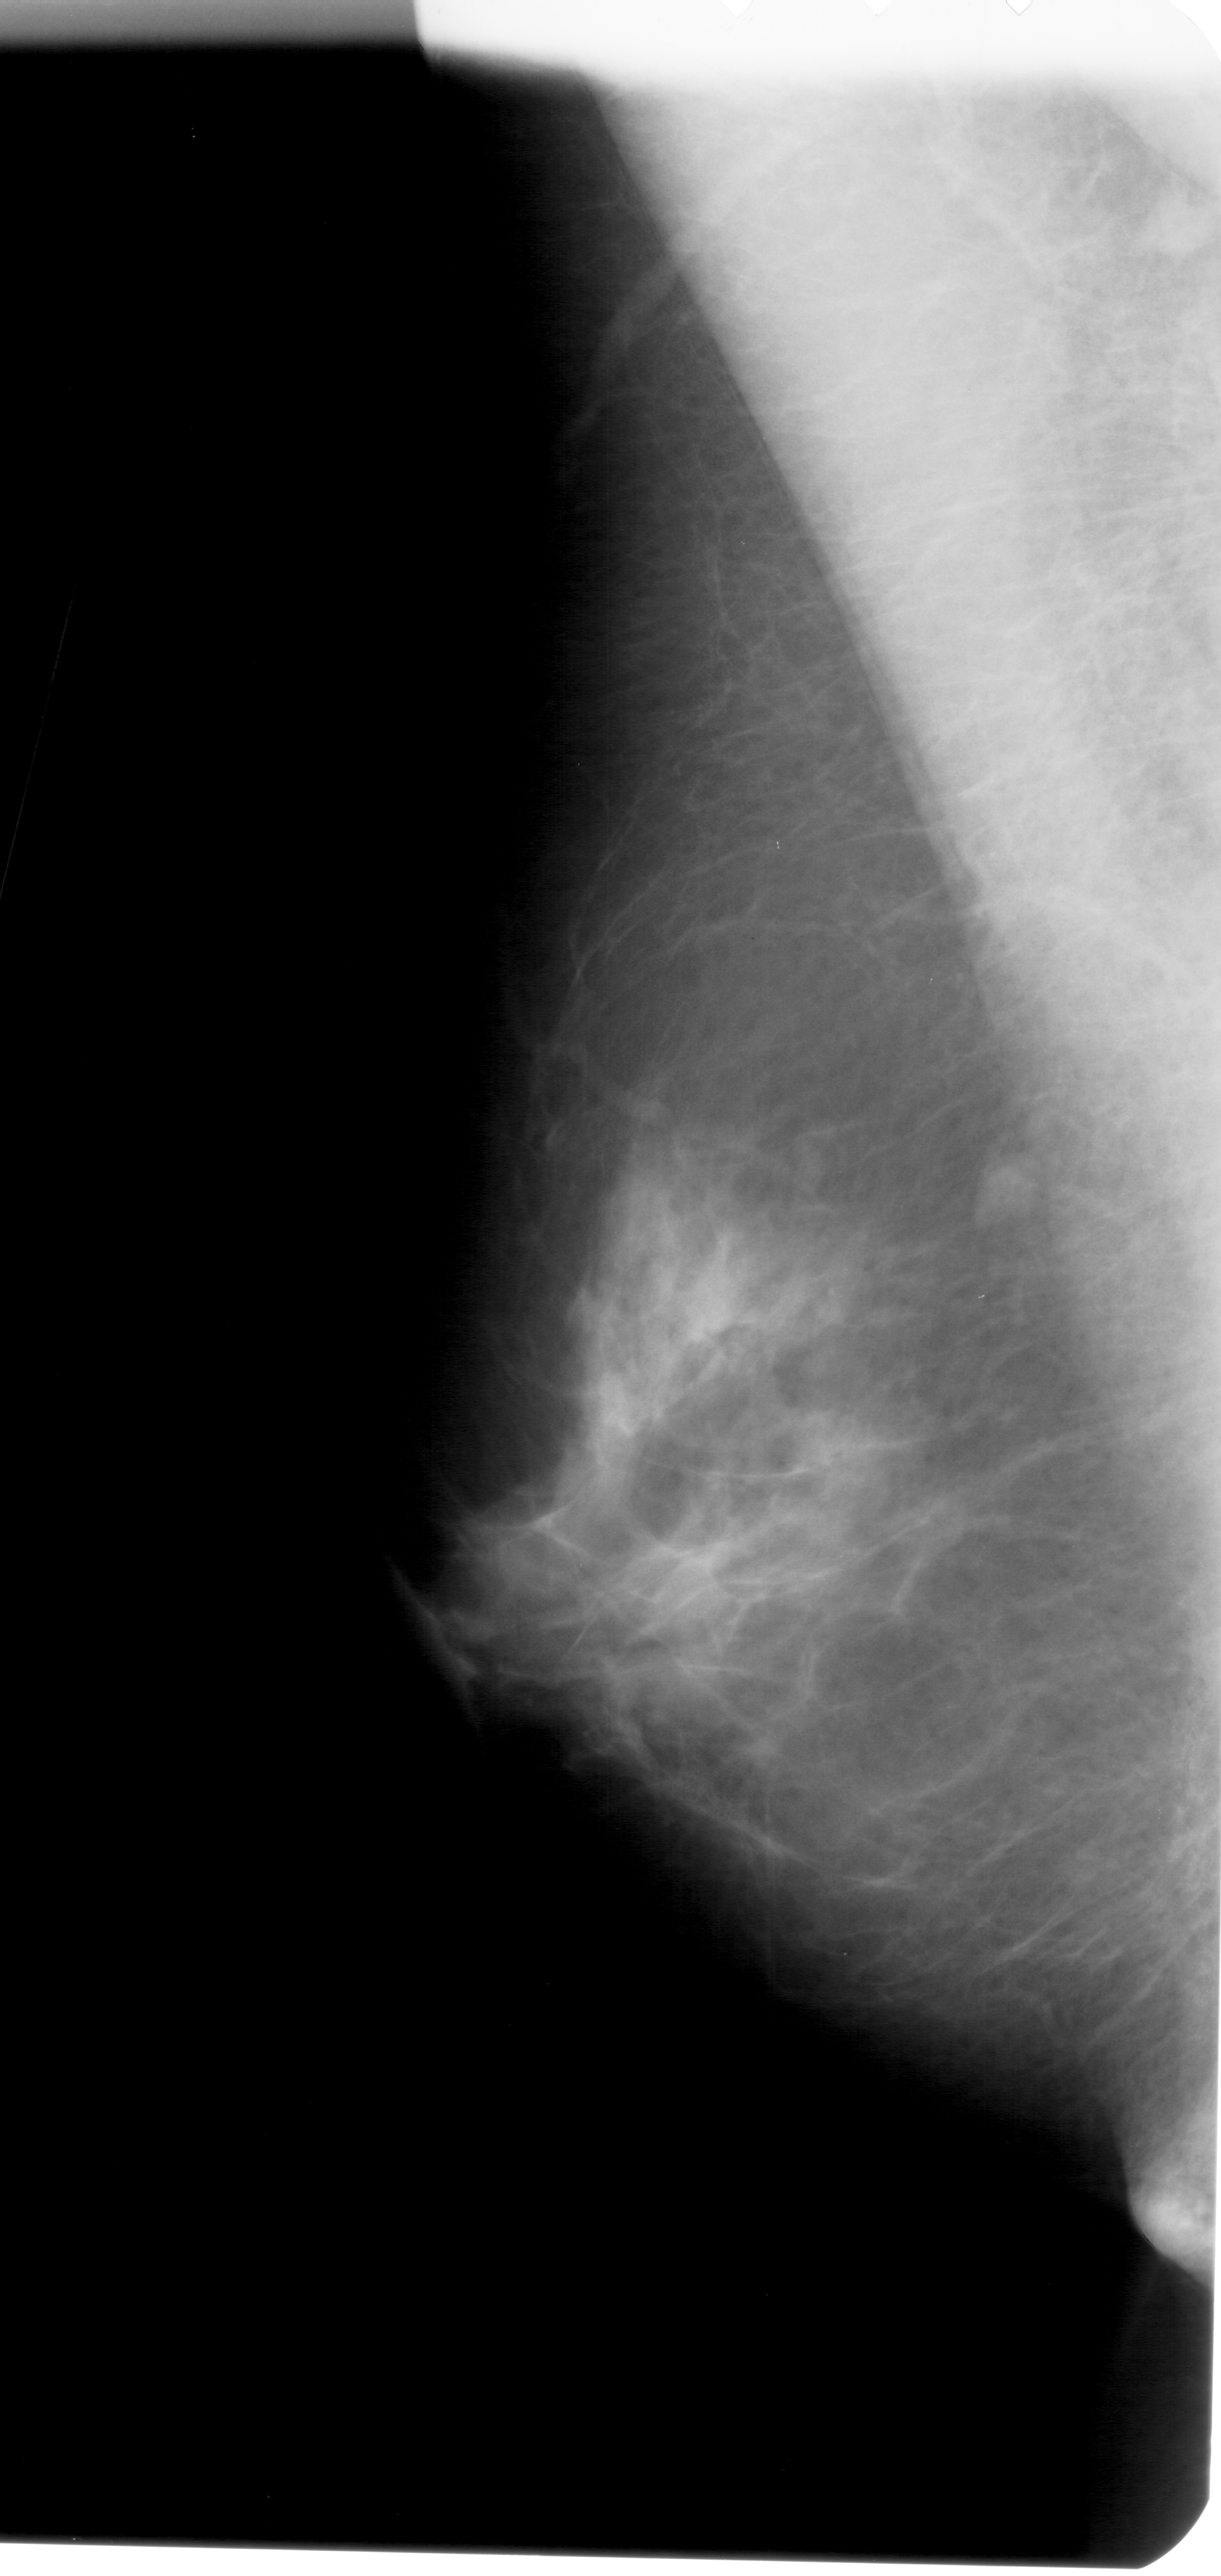
Digitized screen-film mammogram; left breast; mediolateral oblique (MLO) view; breast composition: scattered fibroglandular densities (BI-RADS density category 2 of 4); 1221 × 2576 image matrix.
Expert-marked regions of interest on this image (one box per marked abnormality):
- mass, shape oval, margins circumscribed; BI-RADS assessment category 3; pathology result (as recorded, not read from the image): benign: bounding box (x1, y1, x2, y2) in pixels: (972, 1143, 1036, 1229)